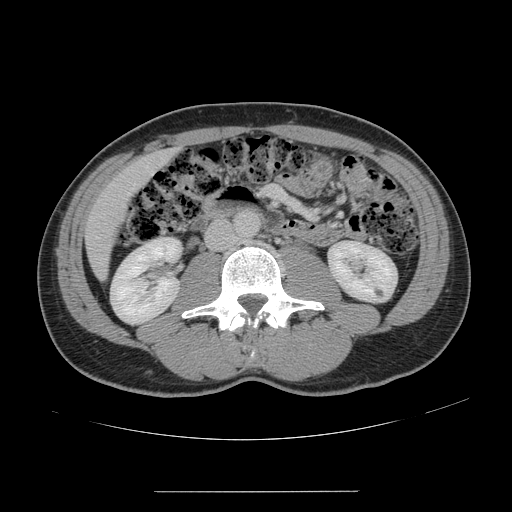
Contrast-enhanced abdominal CT, one axial slice. Slice 41 of 178 in the series (ordered by position). 120 kVp. Intravenous contrast given. Soft-tissue window (W 400 / L 40 HU). 512 × 512 image matrix. Male patient, age 53 years. From the clinical record (not read from this slice): diagnosis: colorectal cancer liver metastases, imaged before liver resection; multiple liver metastases: yes; largest metastasis: 2.4 cm.
Structures marked on this image (outlined manually by an expert reader):
- hepatic veins: bounding box (x1, y1, x2, y2) in pixels: (127, 172, 153, 195)
- liver: (86, 151, 174, 277)